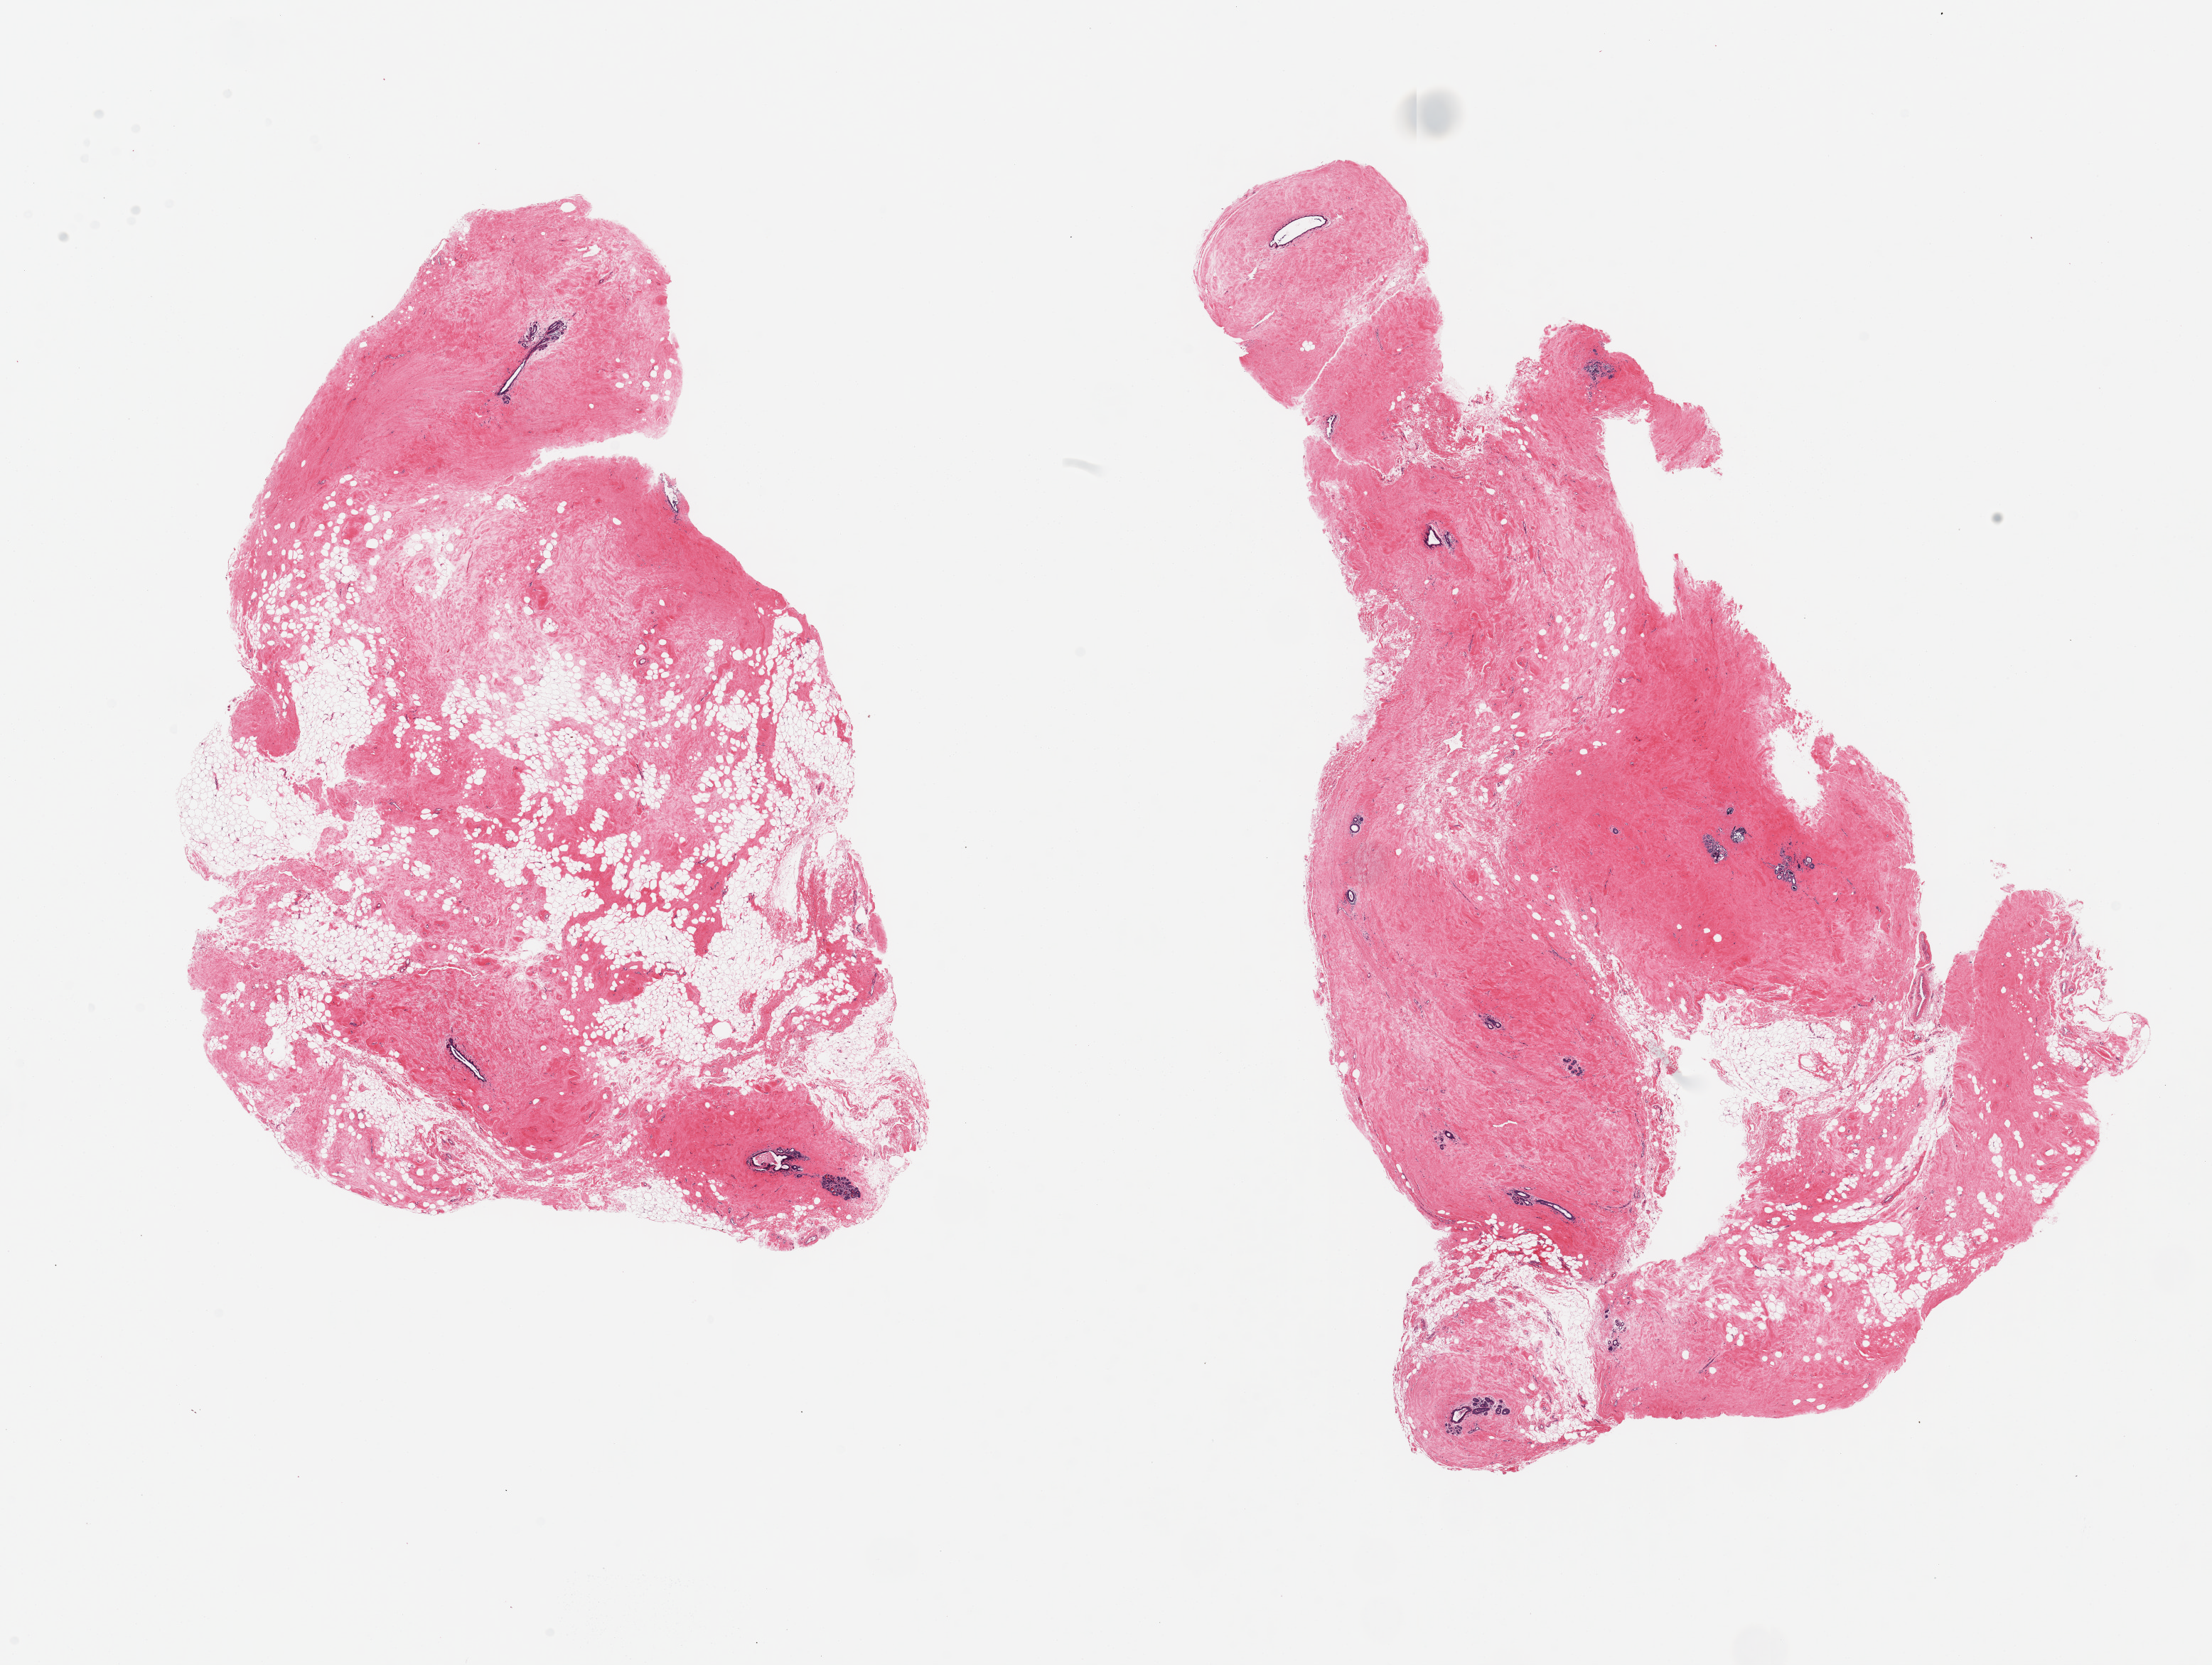
Digitized hematoxylin and eosin (H&E)-stained section — shown as a low-resolution overview of the whole scanned area (about 24.6 x 18.5 mm), PAXgene-fixed, paraffin-embedded tissue, section of breast (target tissue), donor tissue sample. Donor sex: female.
Pathologist's review note for this sample: 2 pieces atrophic TDLUs present.